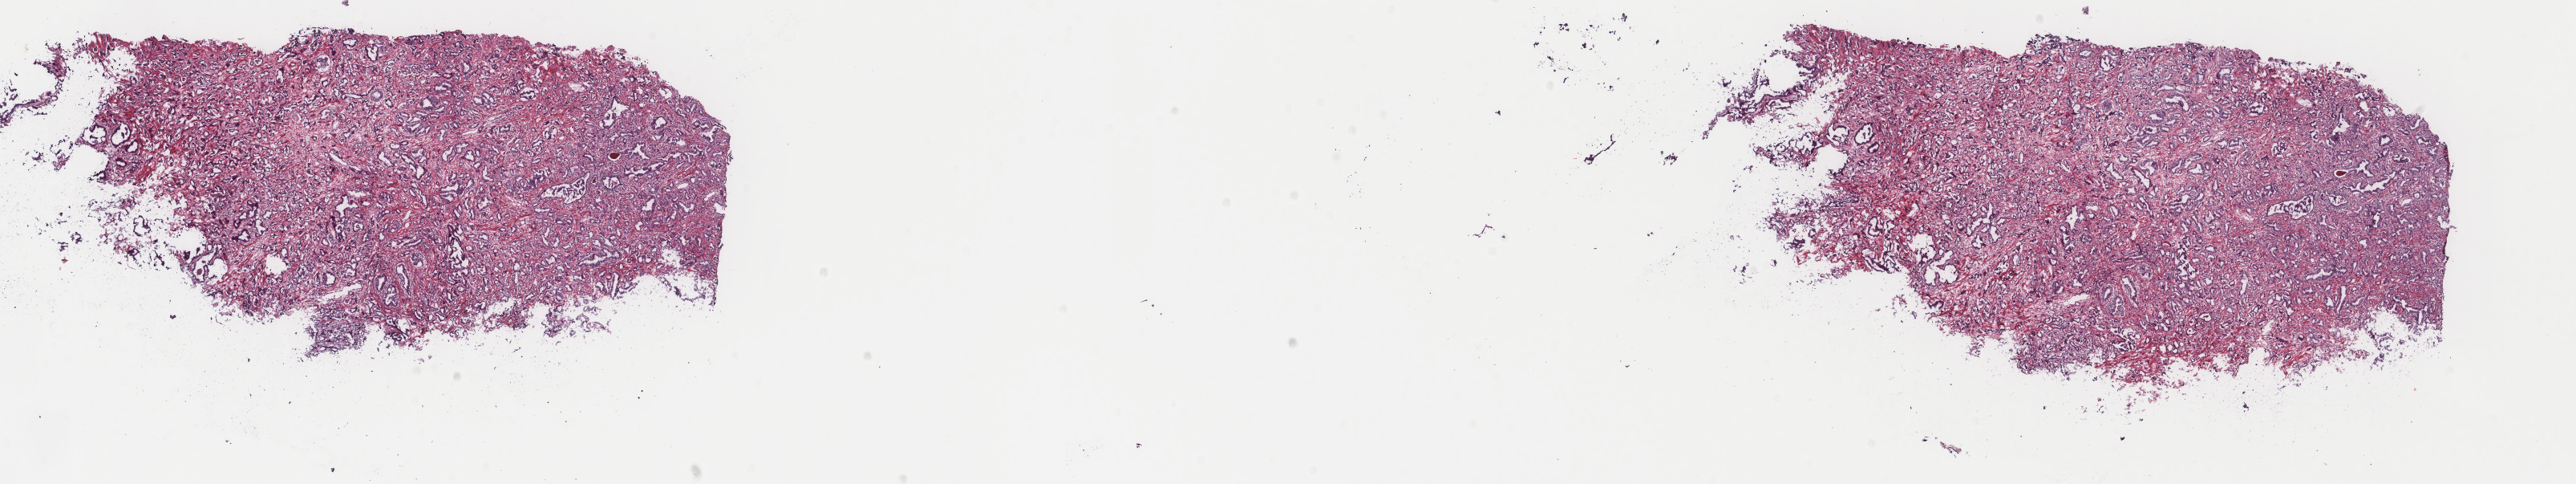
Whole-slide histology image, Hematoxylin and eosin (H&E) stained, a low-resolution overview of the entire scanned area, about 25.5 x 4.8 mm; frozen section from the top of the tissue portion; primary tumour sample from the prostate. Male, age 63 years at initial diagnosis. Gleason score: 7 (4+3). Composition of this section per pathologist review: tumour cells 50%, tumour nuclei 85%, normal cells 0%, stromal cells 48%, necrosis 2%. Inflammatory infiltration, as recorded: lymphocyte infiltration 5%, monocyte infiltration 0%, neutrophil infiltration 0%.
• diagnosis: Adenocarcinoma, NOS (prostate gland)
• lymph nodes positive (case pathology): 0 of 27 examined
• laterality: bilateral